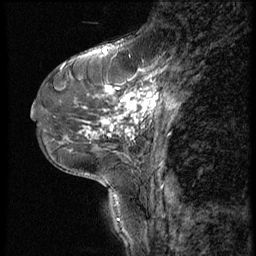
Breast MRI (dynamic contrast-enhanced), one sagittal slice; slice 22 of 56 in the series (ordered by position); 3 images stored at this slice position (order not interpretable as contrast timing); 1.5 T; TE 4.2 ms, TR 9 ms; 256 × 256 image matrix, field of view 180 × 180 mm. Patient: female, 46 years. Case-level facts recorded for this patient, not image findings: setting: breast cancer imaged before/during neoadjuvant chemotherapy; receptor status: HER2-positive.
Annotated regions visible in this slice (semi-automatically segmented with operator editing):
- analysis volume of interest (the breast-tissue region the enhancement analysis was run in; not a lesion): box from (x=79, y=68) to (x=190, y=143) px
- tumour enhancement mask (voxels above the 140 % enhancement threshold inside the analysis volume of interest): (x=85, y=73)–(x=158, y=139)